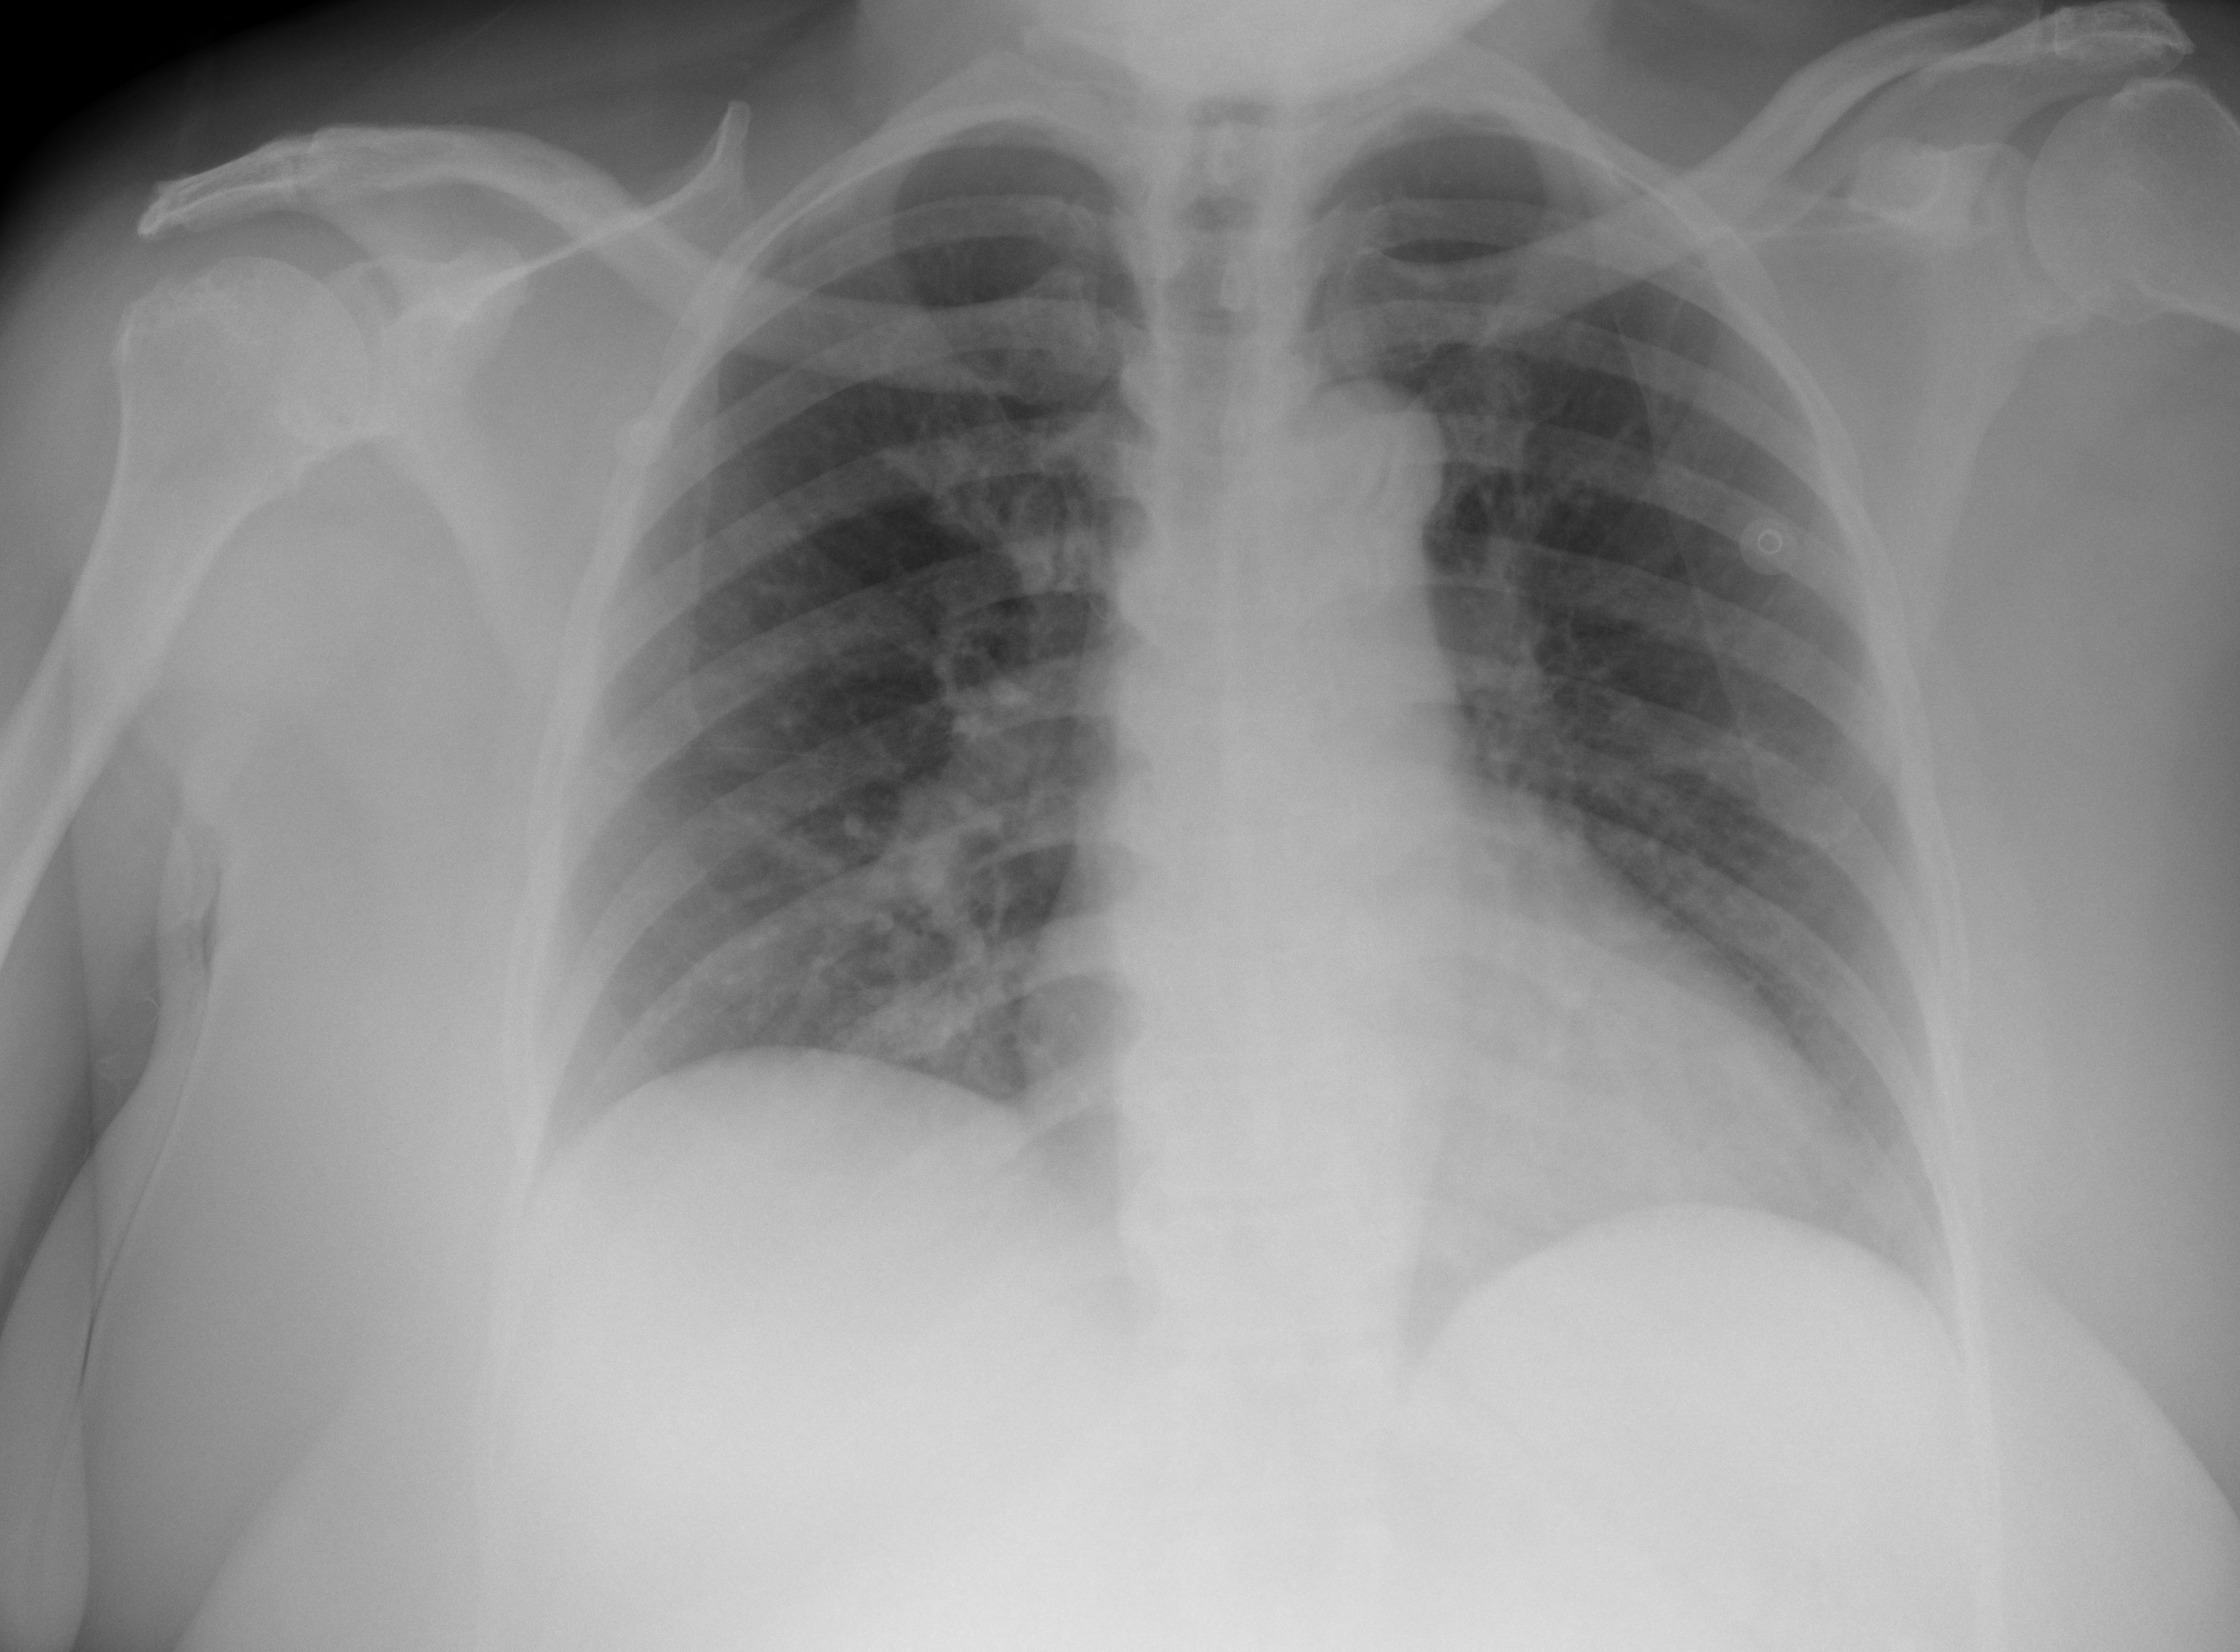
Portable chest radiograph, AP projection. Female patient, age 61 years; COVID-19 (test-positive).
Key findings recorded by the radiologist: No relevant findings.